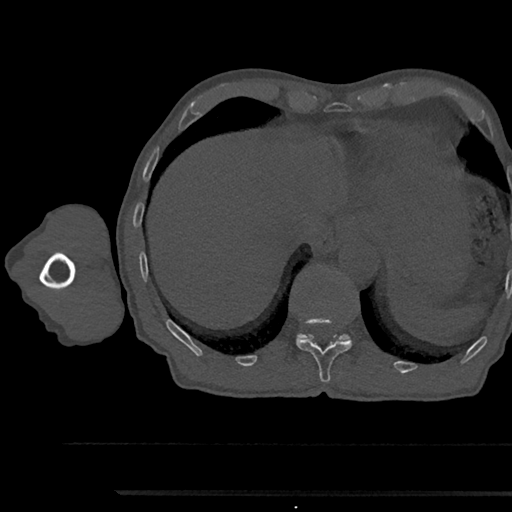
CT including the spine, one axial slice. Slice 765 of 797 in the series (ordered by position). 120 kVp. Bone window (W 1800 / L 400 HU). 0.5 mm slice thickness. 512 × 512 image matrix, field of view 367 × 367 mm. Male patient, age 79 years. From the clinical record (not read from this slice): primary cancer: prostate.
Annotated regions visible in this slice (semi-automatically segmented with operator editing):
- T11 vertebra: box from (x=296, y=319) to (x=352, y=383) px
- T12 vertebra: (x=297, y=333)–(x=351, y=341)